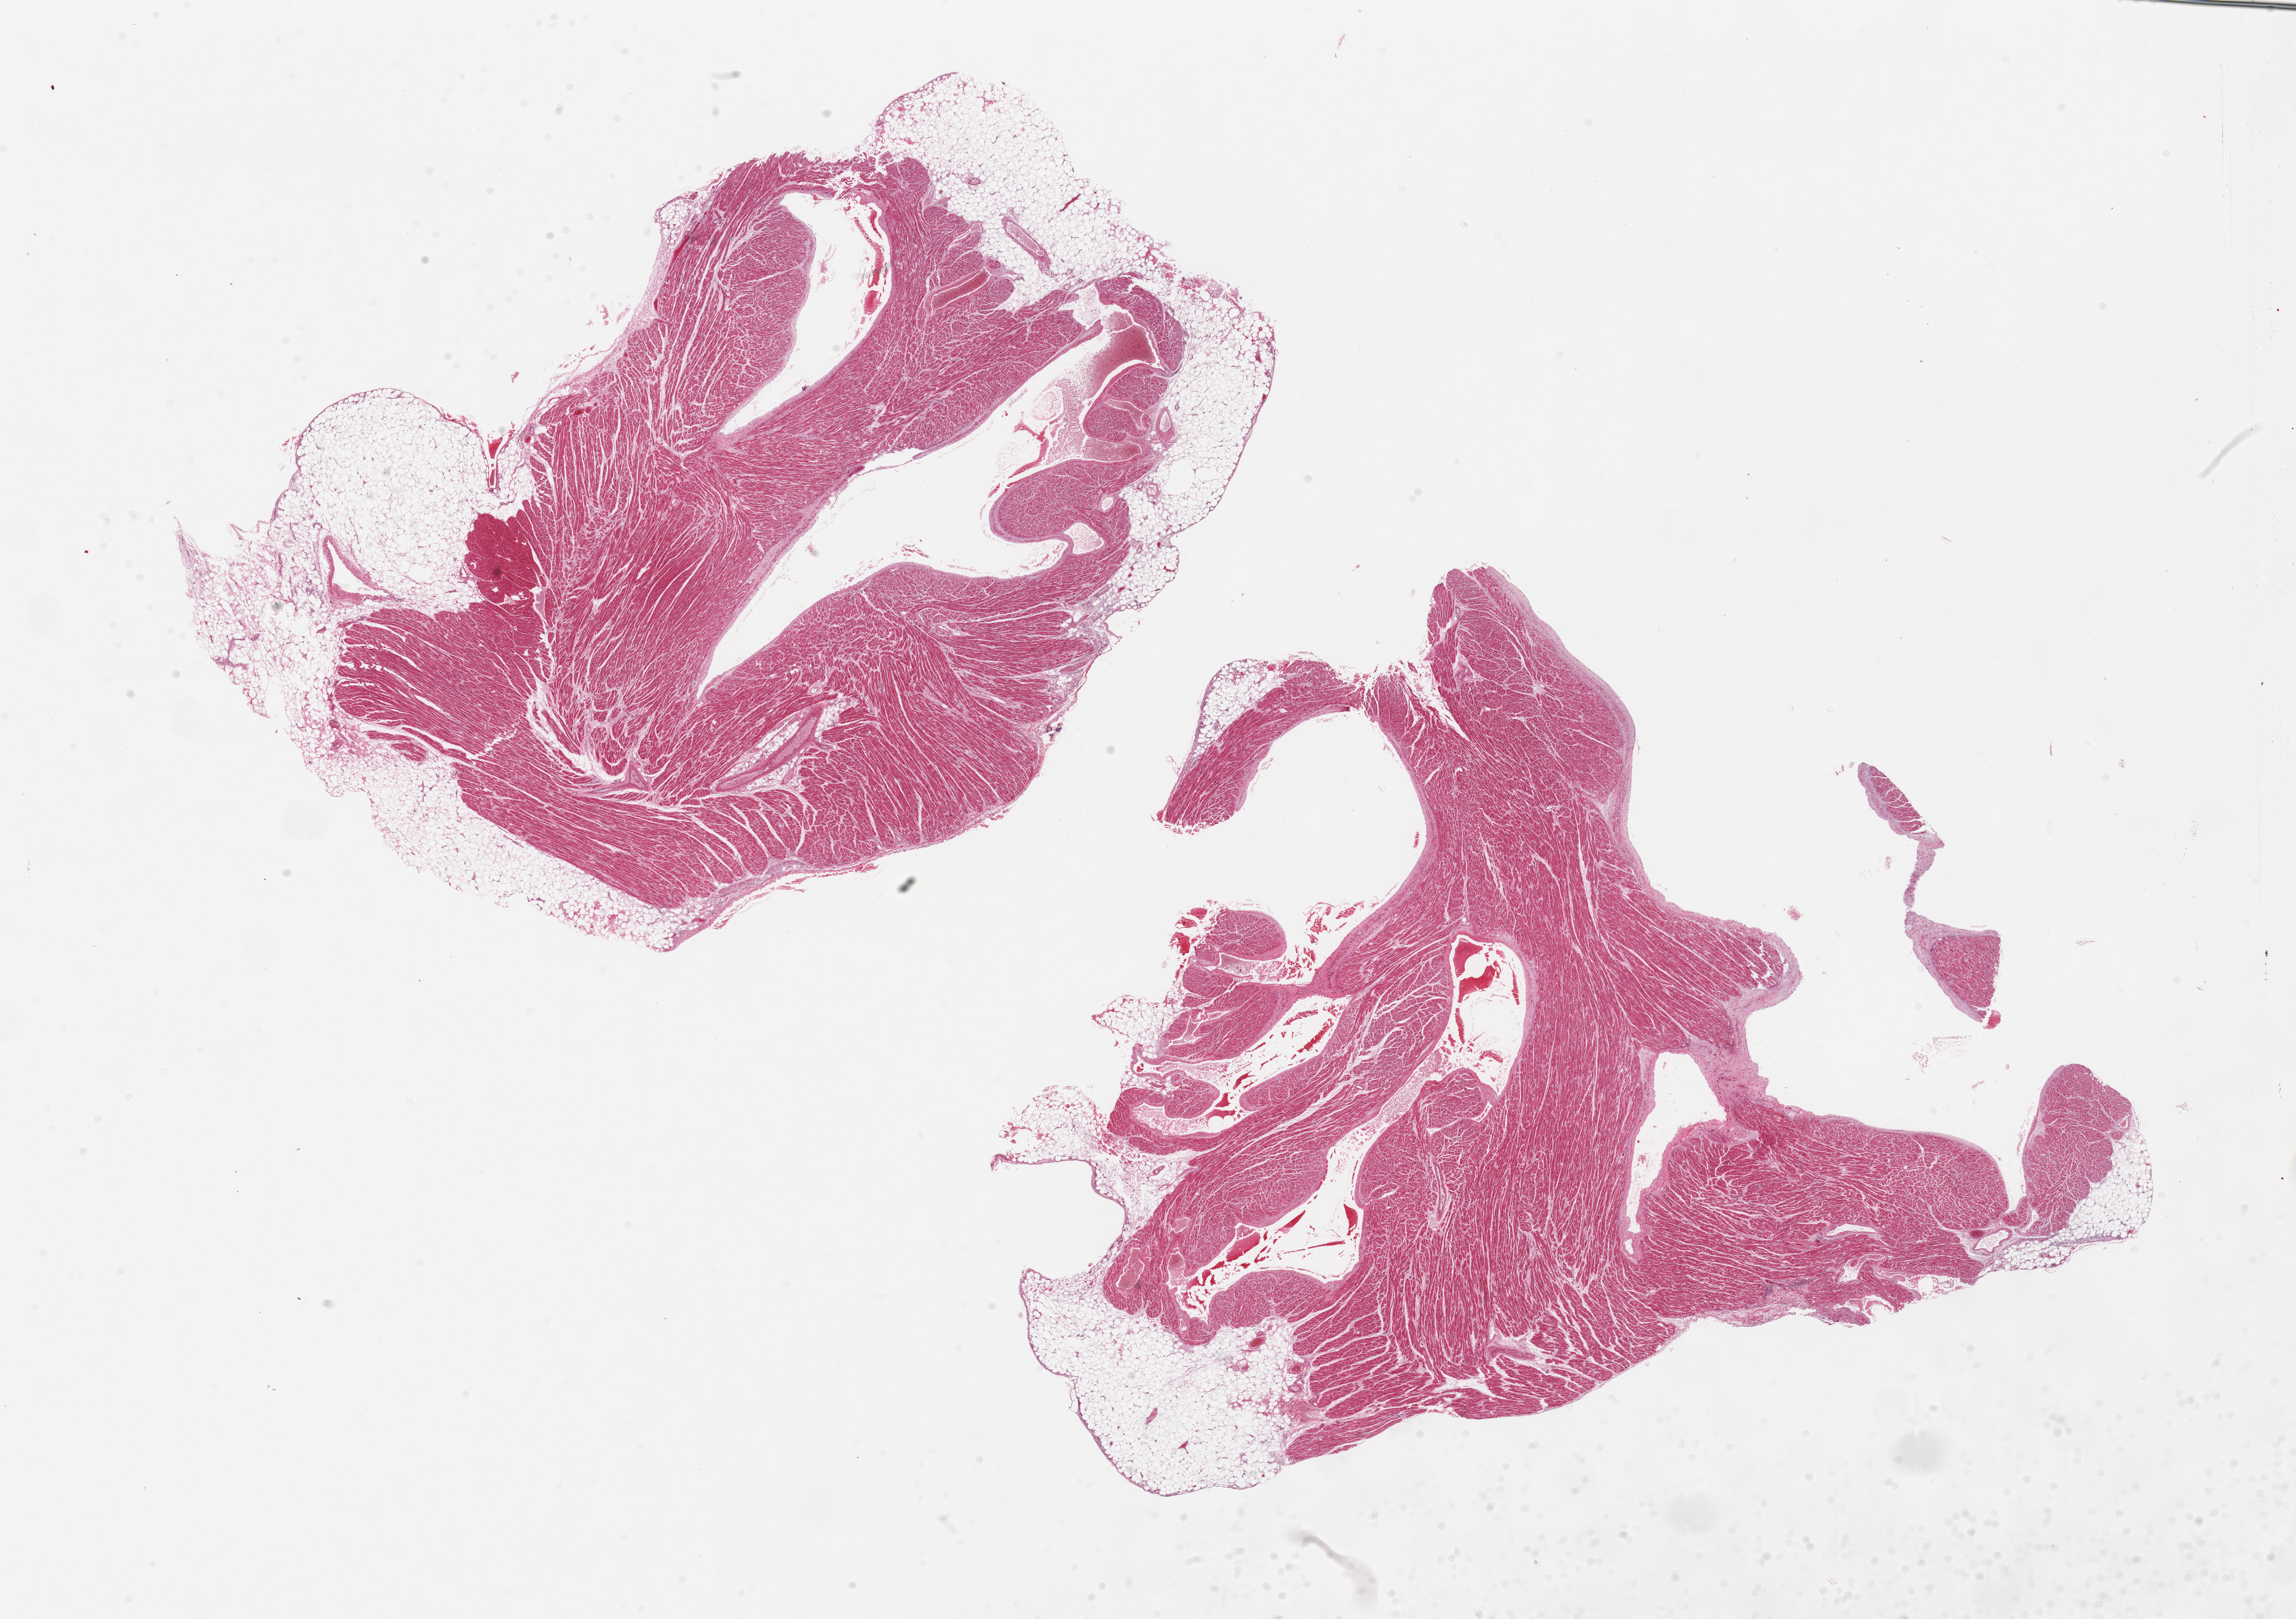
Digitized hematoxylin and eosin (H&E)-stained section, low-resolution overview of the scanned area, about 29.5 x 20.8 mm, PAXgene-fixed, paraffin-embedded tissue, section of auricular appendage (target tissue), donor tissue sample. Donor: male.
Pathologist's review note for this sample: 2 pieces, no abnormalities.